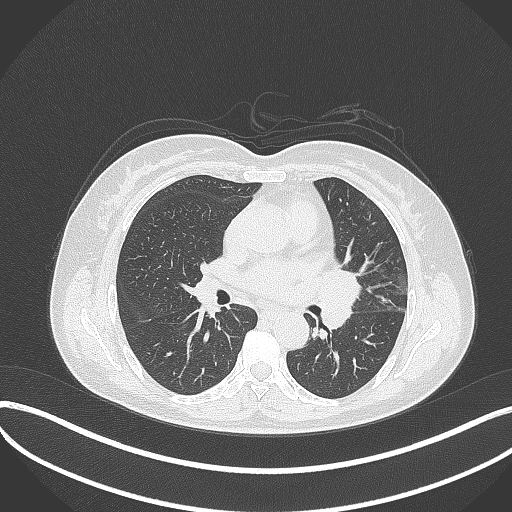
Chest CT, one axial slice. Position 188 of 373 along the scan axis. Reconstruction kernel B70f. 120 kVp. Lung window (W 1500 / L -600 HU). 1 mm slice thickness. 512 × 512 image matrix, field of view 400 × 400 mm. Female patient, age 54 years. Case-level facts recorded for this patient, not image findings: clinical TNM (as recorded): T2a N1 M0.
Structures marked on this image (bounding box drawn by a radiologist):
- lung tumour (recorded histology: small cell carcinoma): bounding box <316,266,365,337> (left, top, right, bottom; pixels)